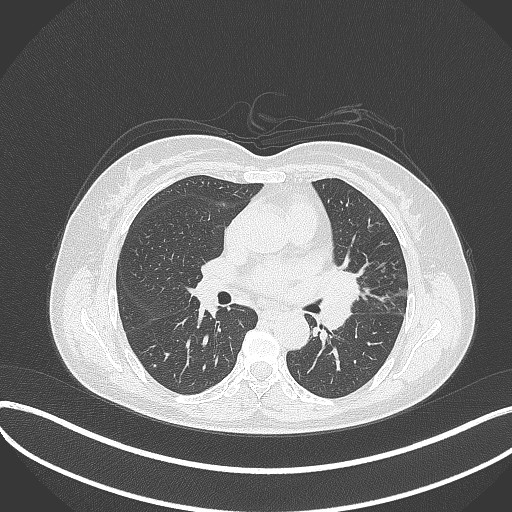
Chest CT, one axial slice; slice 190 of 373 in the series (ordered by position); 120 kVp; lung window (W 1500 / L -600 HU); 1 mm slice thickness; 512 × 512 image matrix, field of view 400 × 400 mm. Female patient, age 54 years. From the clinical record (not read from this slice): clinical TNM (as recorded): T2a N1 M0; histopathological grade: G3.
Annotated regions visible in this slice (rectangle marked by the reading radiologist):
- lung tumour (recorded histology: small cell carcinoma): bounding box [x1, y1, x2, y2] px = [319, 264, 364, 332]